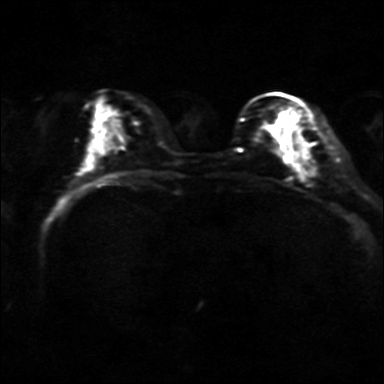
Breast MRI, one axial slice; position 15 of 36 along the scan axis; diffusion-weighted series; image 2 of 4 stored at this slice position (different b-values; order by instance number); 3 T; 4 mm slice thickness; 384 × 384 image matrix, field of view 320 × 320 mm. Female patient.
Outlined on this slice (manually delineated by an expert):
- tumour on diffusion-weighted imaging: box from (x=291, y=152) to (x=300, y=168) px